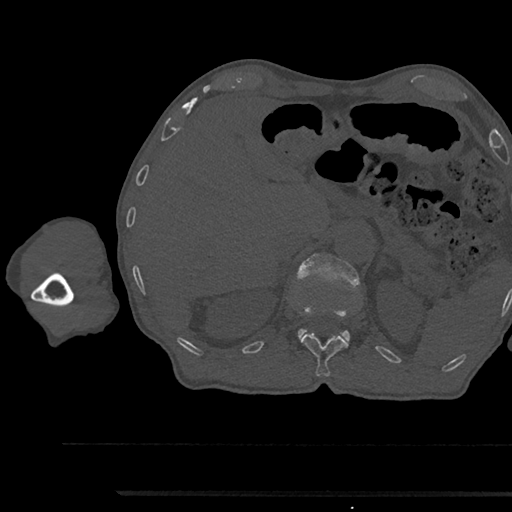
CT including the spine, one axial slice. Reconstruction kernel Br40s/3. 120 kVp. Bone window (W 1800 / L 400 HU). 0.5 mm slice thickness. 512 × 512 image matrix, field of view 367 × 367 mm. Patient: male, 79 years. From the clinical record (not read from this slice): primary cancer: prostate.
Annotated regions visible in this slice (semi-automatic segmentation, software-assisted and operator-edited):
- L1 vertebra: bounding box [x1, y1, x2, y2] px = [295, 254, 360, 342]
- T12 vertebra: [301, 333, 349, 377]